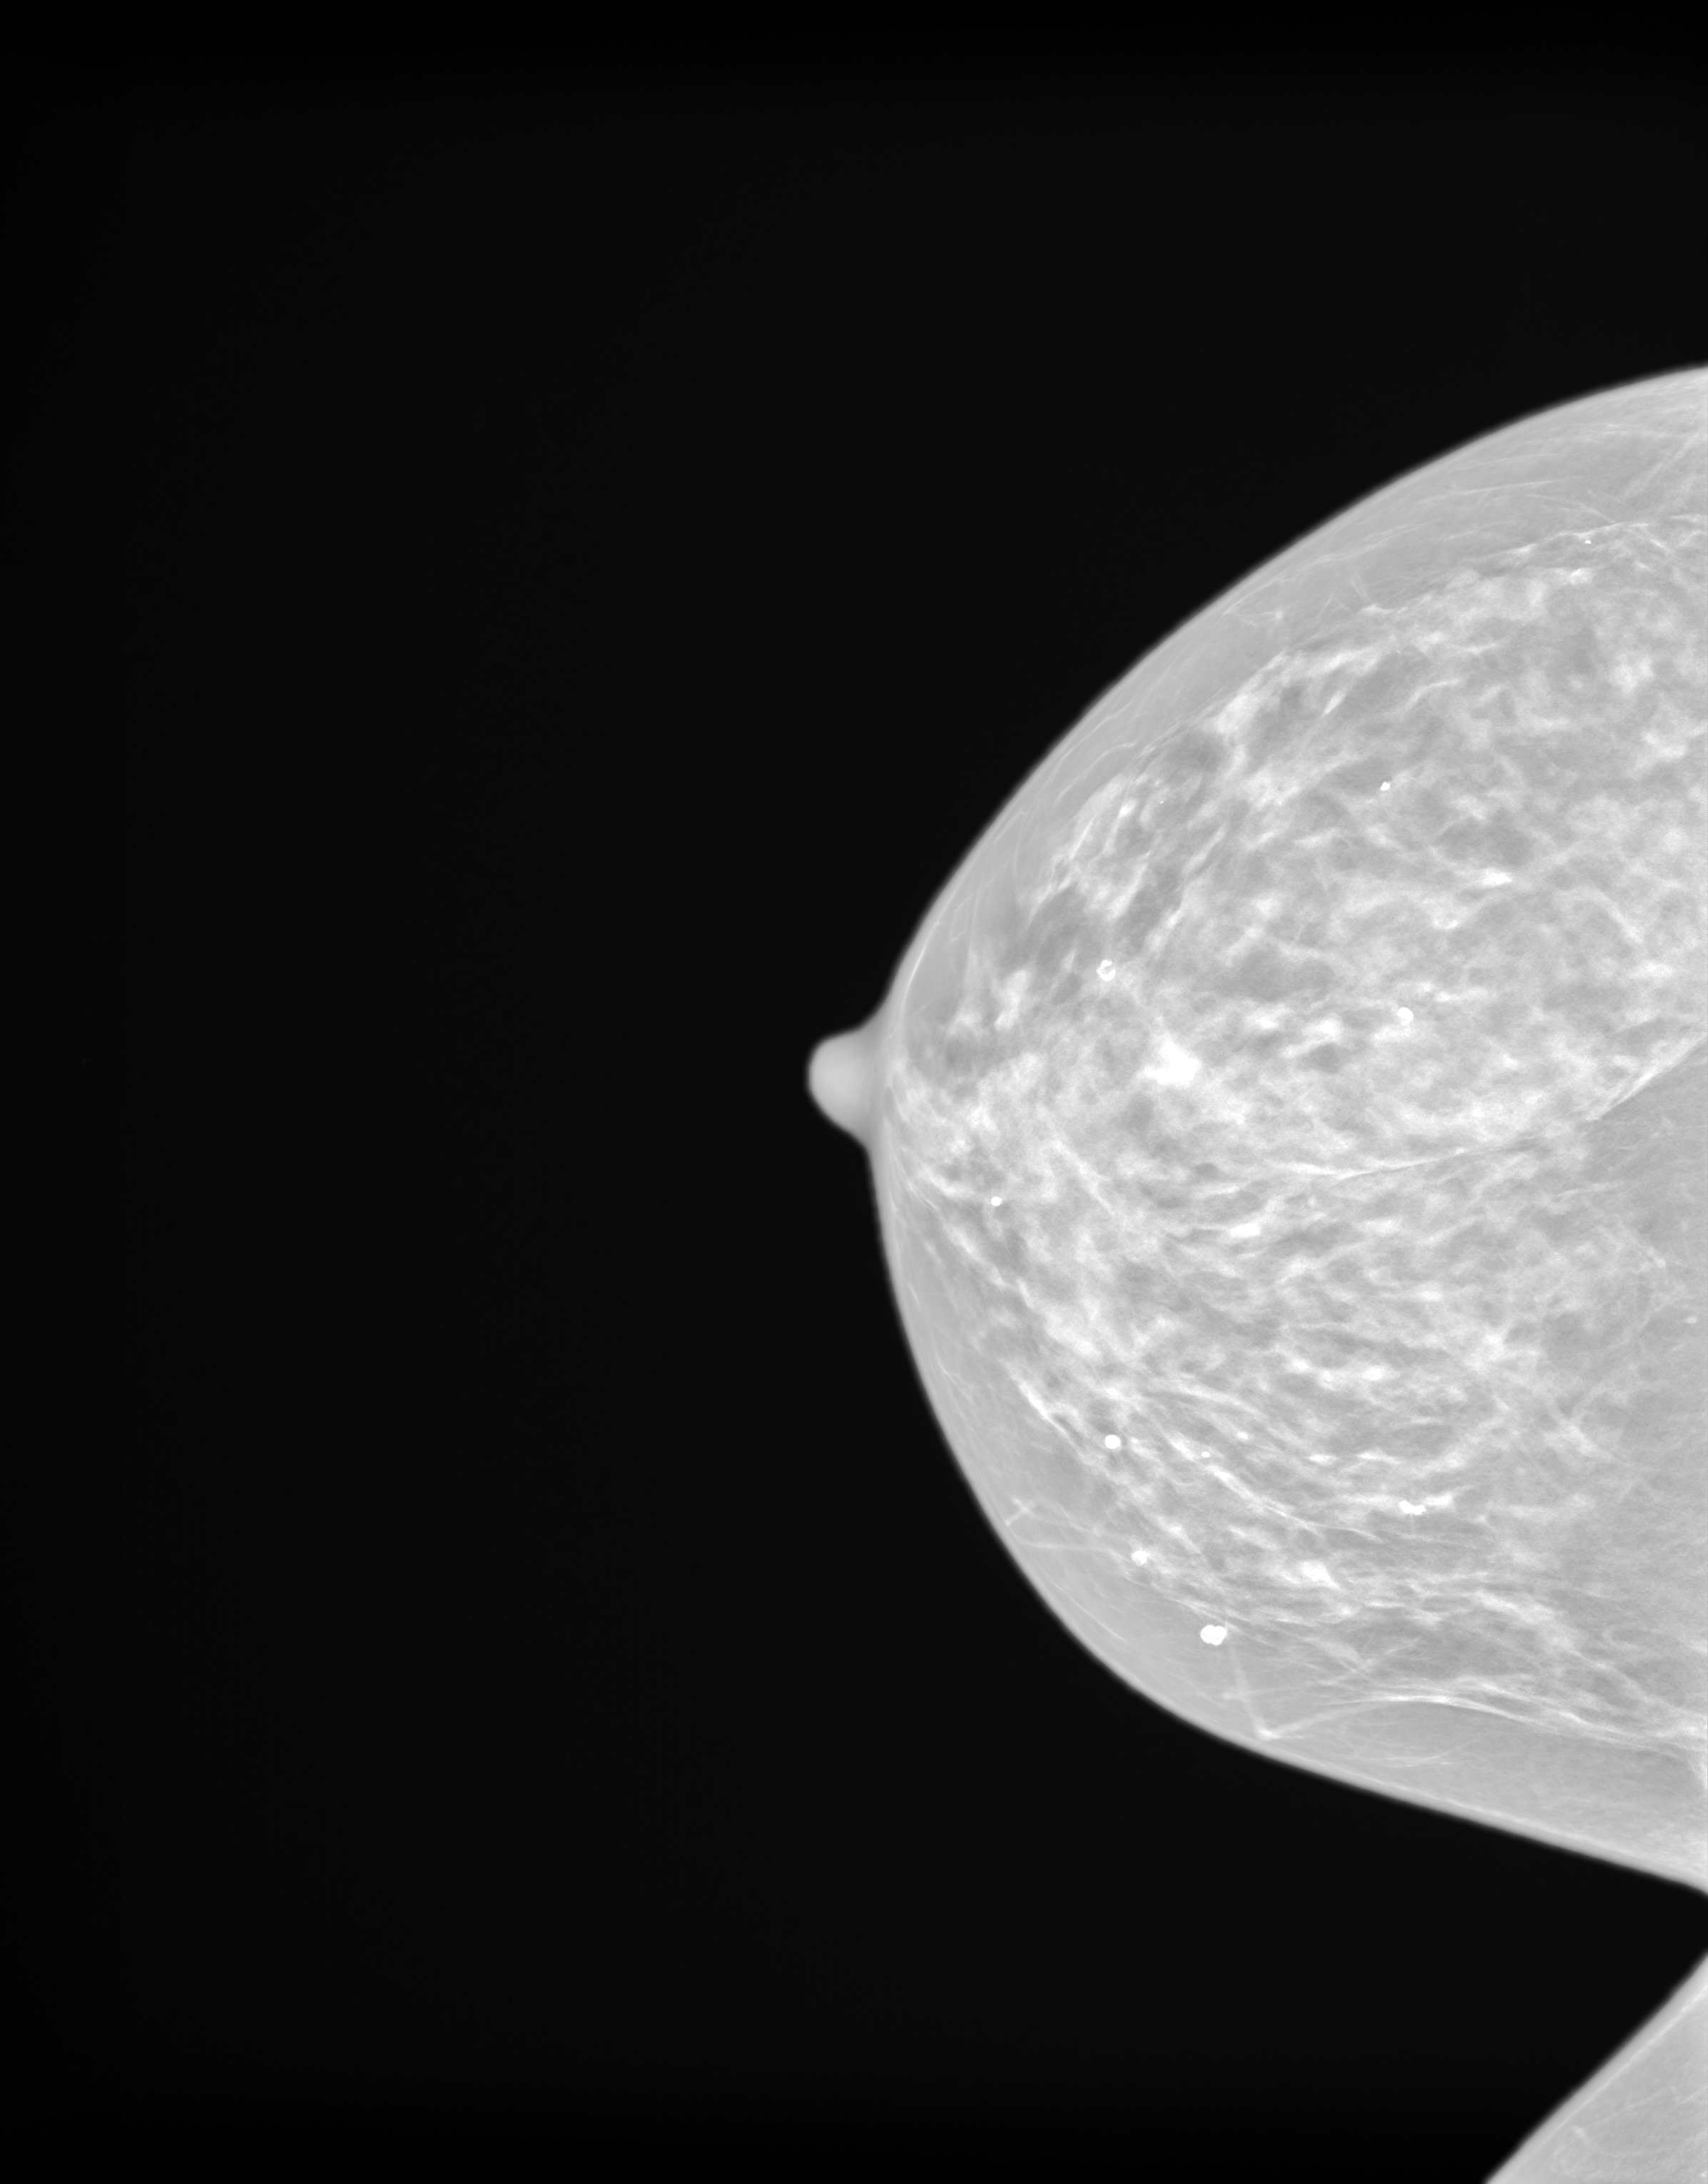
Synthetic 2-D view generated from a tomosynthesis acquisition (not an FFDM exposure), right breast, CC view, annual screening mammography examination. Patient: female, 66 years.
BI-RADS breast density category at the screening exam (both breasts, scale 1–4): 3. Final BI-RADS category for the screening round (tomosynthesis exam, both breasts): category 1. Recall: no recall after this screen.